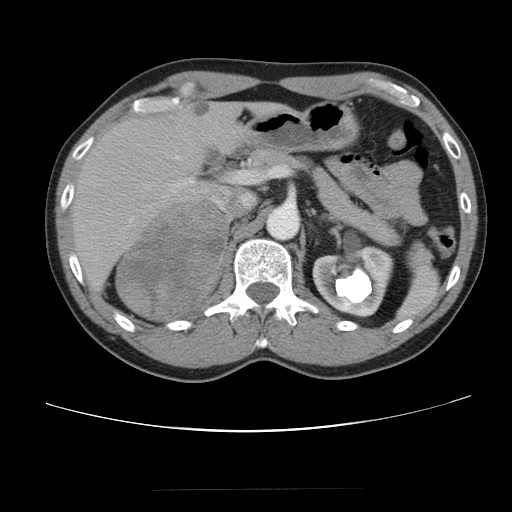
Contrast-enhanced abdominal CT, one axial slice. Reconstruction kernel STANDARD. 120 kVp. Intravenous contrast given. Soft-tissue window (W 400 / L 40 HU). 5 mm slice thickness. 512 × 512 image matrix. Patient: male, 61 years. From the clinical record (not read from this slice): diagnosis: adrenocortical carcinoma; tumour side: right adrenal; tumour size at pathology: 11.1 cm; Ki-67 index: 32 %; stage (as recorded): 2.
Outlined on this slice (semi-automatic segmentation, software-assisted and operator-edited):
- mass: bounding box [x1, y1, x2, y2] px = [117, 203, 227, 317]